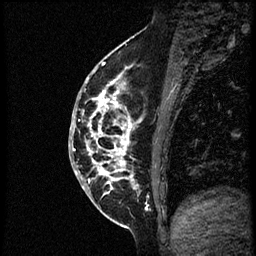
Breast MRI (dynamic contrast-enhanced), one sagittal slice. Position 24 of 56 along the scan axis. Dynamic contrast-enhanced study with each time point stored as its own series, time point 2 of 3 at this slice position (early post-contrast, ordered by acquisition time). 1.5 T. TE 4.2 ms, TR 21.3 ms. 2 mm slice thickness. 256 × 256 image matrix, field of view 200 × 200 mm. Female patient, age 41 years. Case-level facts recorded for this patient, not image findings: setting: breast cancer imaged before/during neoadjuvant chemotherapy; receptor status: HER2-positive.
Structures marked on this image (semi-automatically segmented with operator editing):
- analysis volume of interest (the breast-tissue region the enhancement analysis was run in; not a lesion): bounding box <70,73,177,205> (left, top, right, bottom; pixels)
- tumour enhancement mask (voxels above the 100 % enhancement threshold inside the analysis volume of interest): <73,74,137,189>